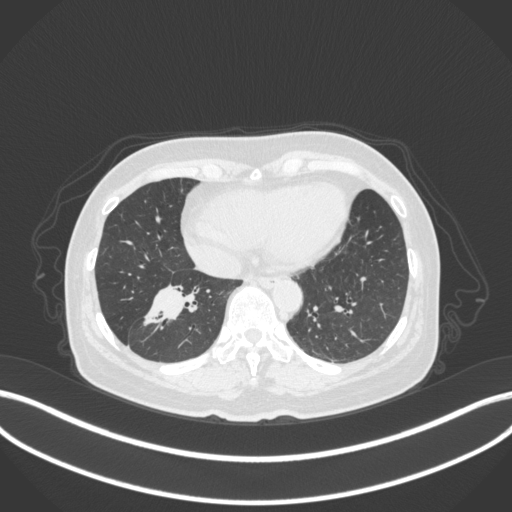
Chest CT, one axial slice; position 127 of 429 along the scan axis; 120 kVp; lung window (W 1500 / L -600 HU); 1 mm slice thickness; 512 × 512 image matrix. Patient: female, 67 years. From the clinical record (not read from this slice): clinical TNM (as recorded): T1c N1 M0; histopathological grade: G2-3.
Structures marked on this image (rectangle marked by the reading radiologist):
- lung tumour (recorded histology: adenocarcinoma): box from (x=139, y=275) to (x=207, y=334) px